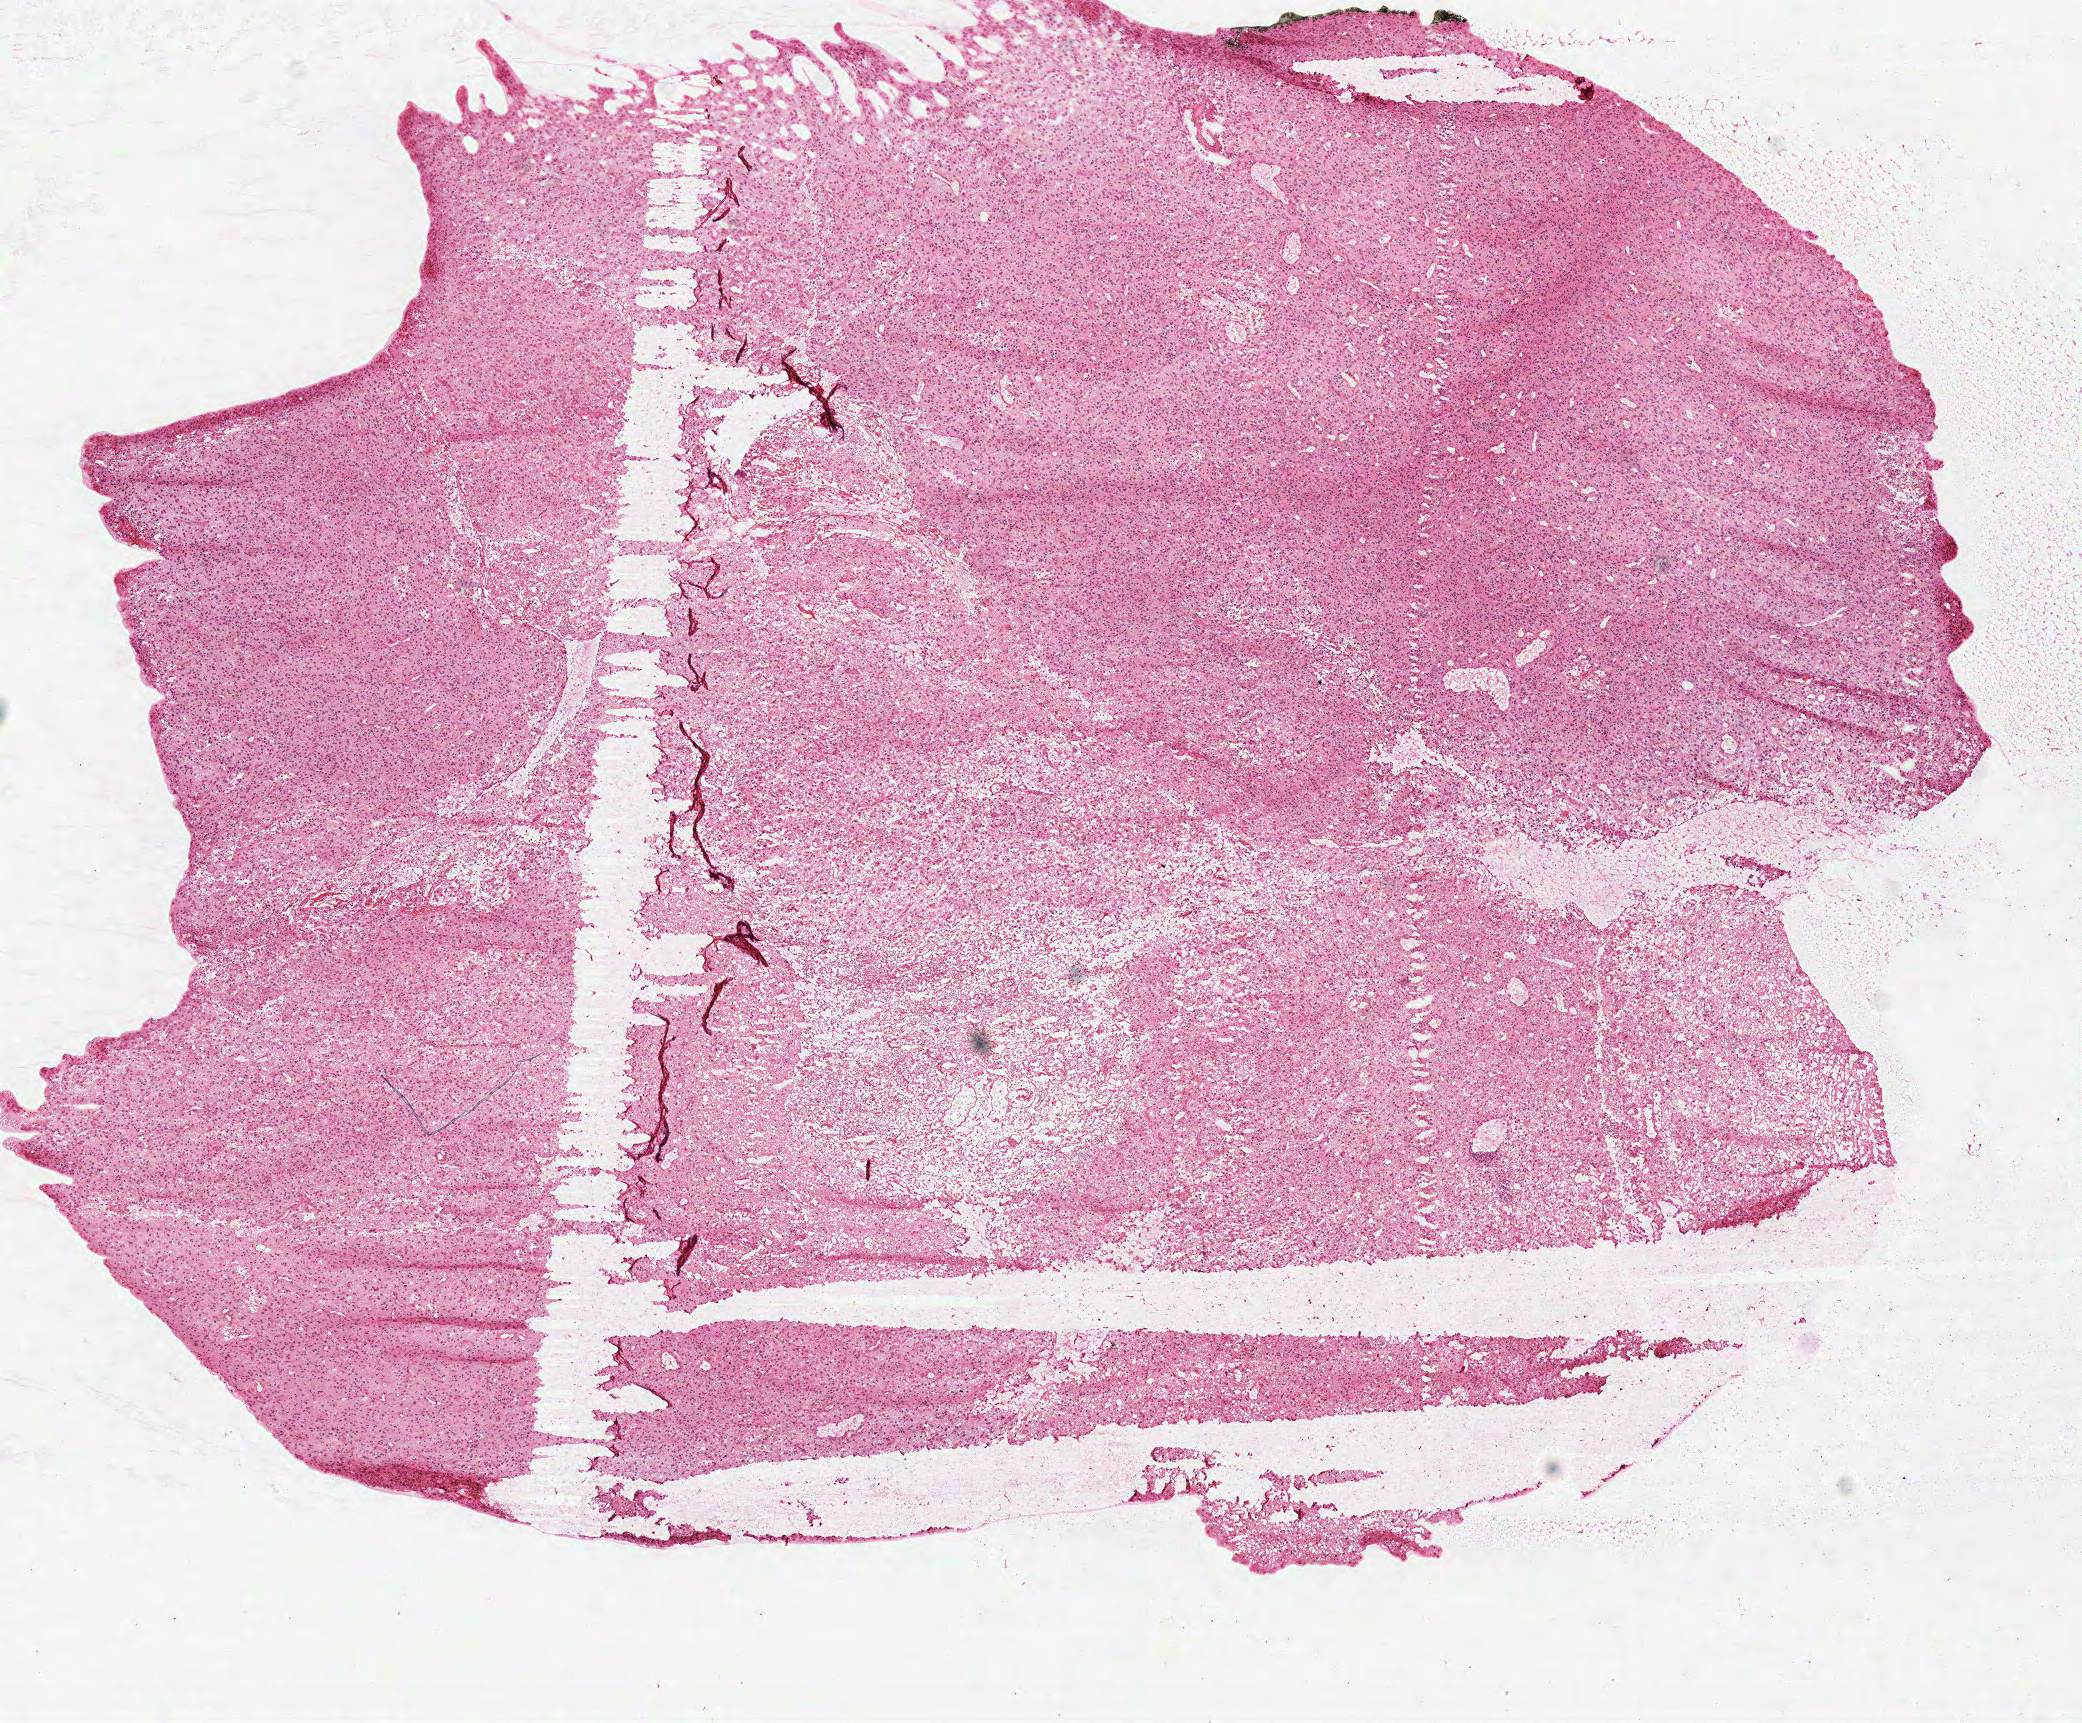
Whole-slide histology image, Hematoxylin and eosin (H&E) stained, shown as a low-resolution overview of the whole scanned area (about 8.2 x 6.8 mm). Frozen section from the top of the tissue portion. Primary tumour sample from the brain. Patient: male, age at initial diagnosis 58 years. Slide review estimates, as recorded: tumour cells 80%, tumour nuclei 80%, normal cells 0%, stromal cells 0%, necrosis 20%.
• histologic diagnosis: Glioblastoma